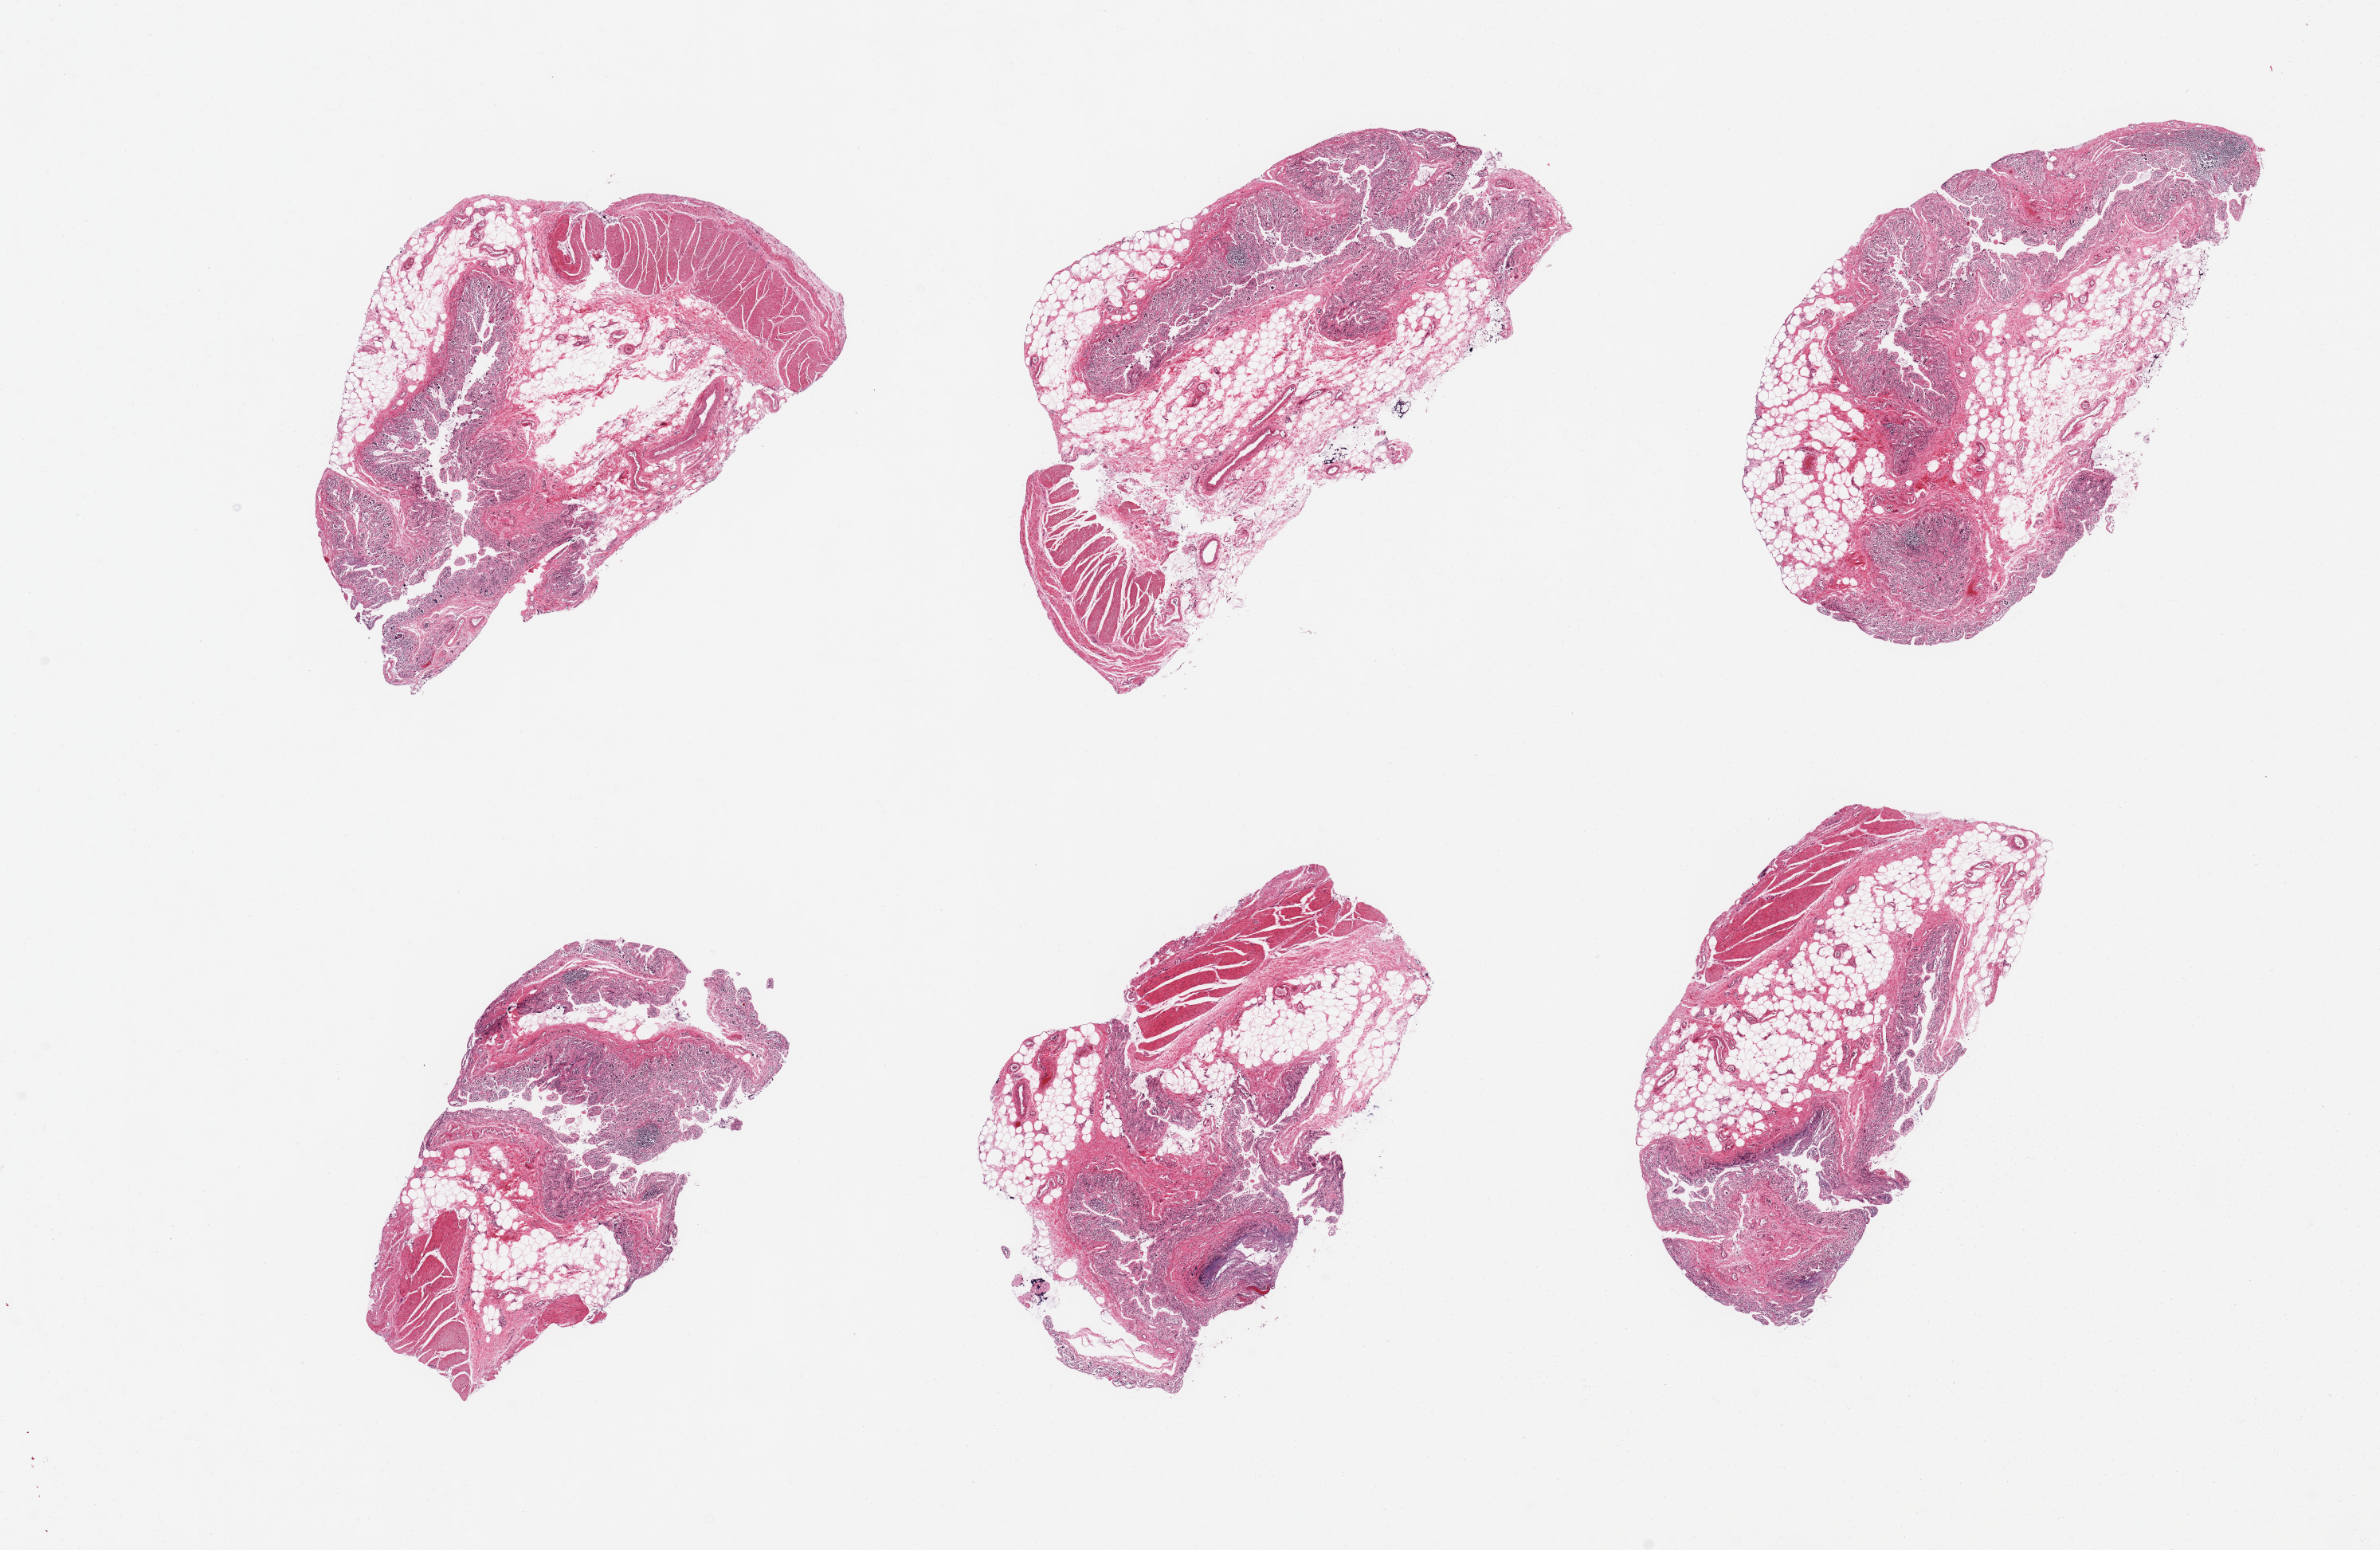
Whole-slide image, H&E stain — whole scanned area (about 23.6 x 15.4 mm, acquisition: 20x scan) shown as a low-resolution overview. PAXgene-fixed, paraffin-embedded tissue. Sampled site (target tissue): ileum. Tissue donor sample. Male donor.
Reviewer comment on this tissue sample: 6 pieces, advanced autolysis in target mucosa; no target lymphid aggregates.